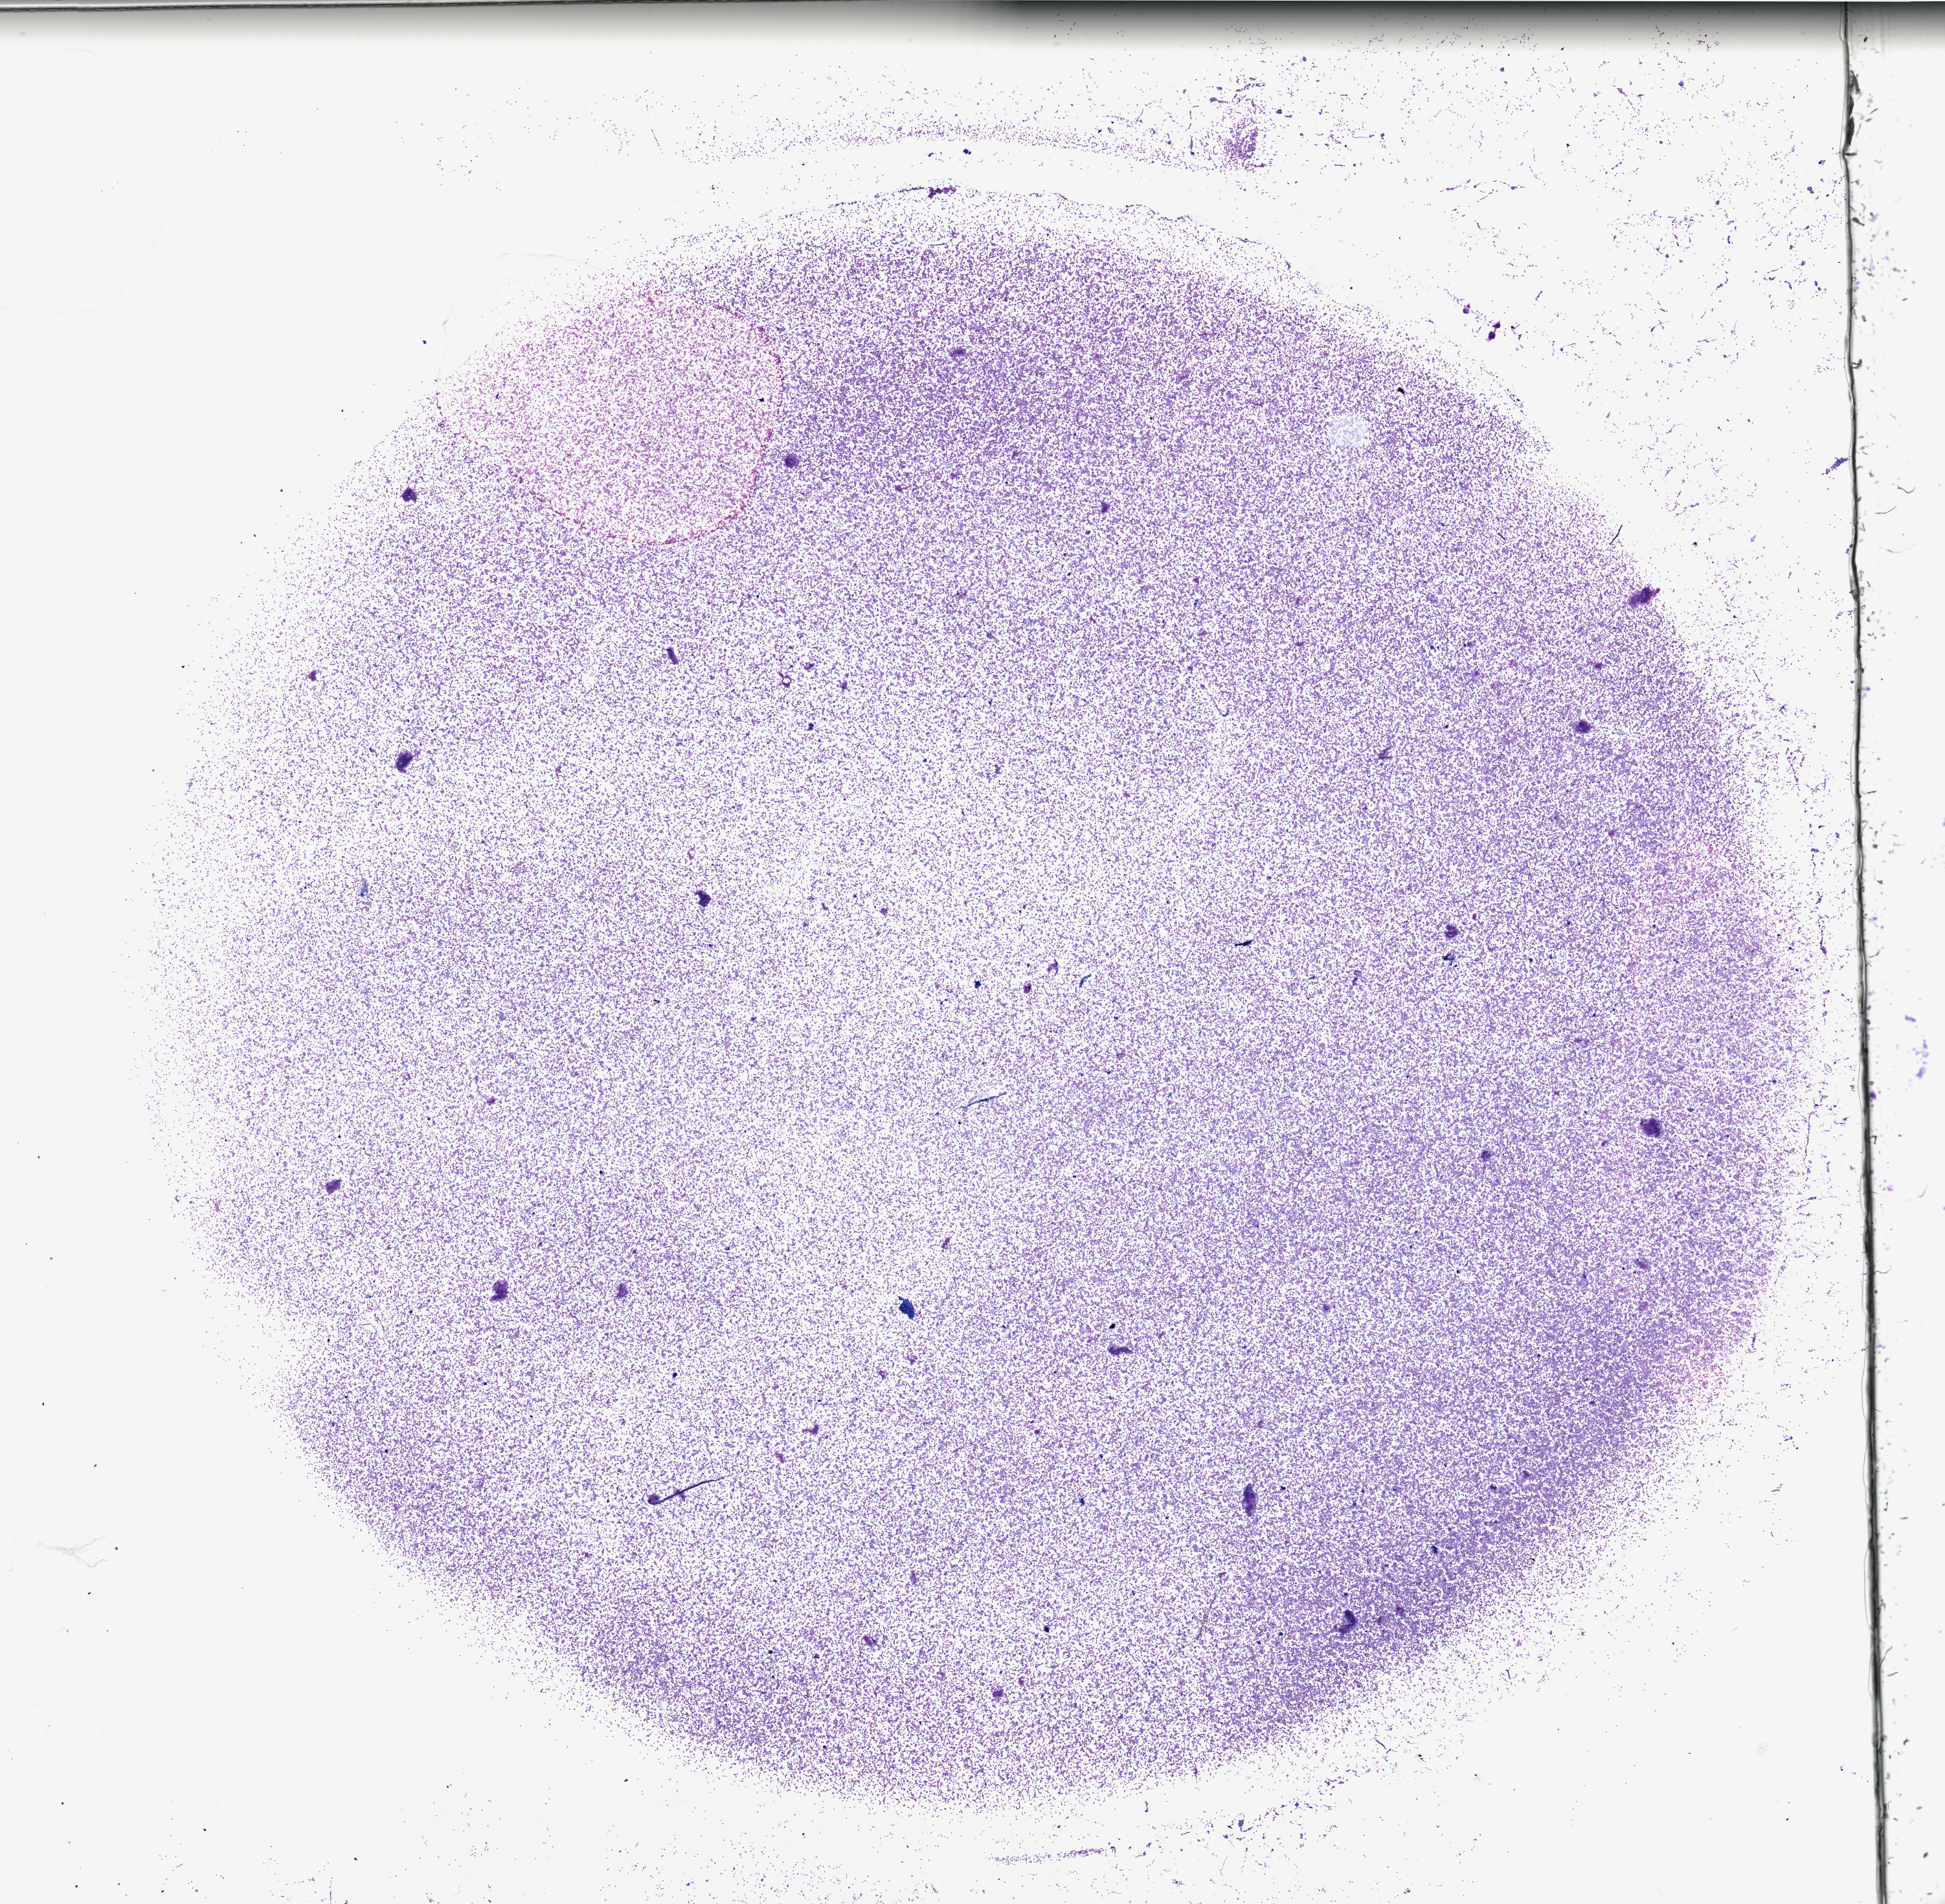
H&E-stained whole-slide image, shown as a low-resolution overview of the whole scanned area (about 23.7 x 23.2 mm, slide scanned at 40x); bone marrow (leukaemic) sample. Patient: female, age 65 years. Blasts: 95%.
WHO classification: AML with t(8;21)(q22;q22); RUNX1-RUNX1T1. Diagnosis: Acute Myeloid Leukemia. FAB classification: M2.